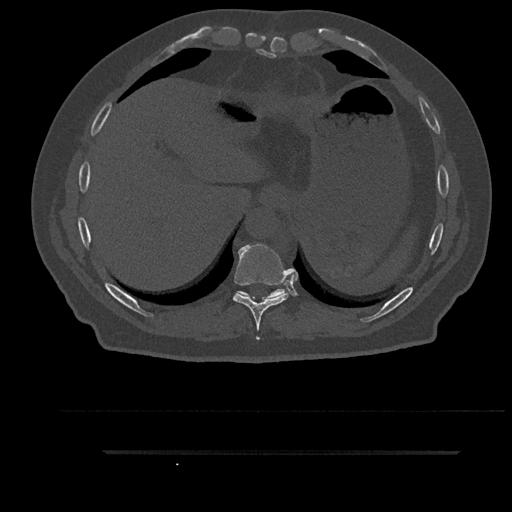
CT including the spine, one axial slice; slice 410 of 797 in the series (ordered by position); bone window (W 1800 / L 400 HU); 0.5 mm slice thickness; 512 × 512 image matrix. Male patient, age 63 years. From the clinical record (not read from this slice): primary cancer: renal; vertebrae with lytic lesions (as recorded): T8.
Annotated regions visible in this slice (semi-automatically segmented with operator editing):
- T10 vertebra: box from (x=237, y=289) to (x=286, y=299) px
- T9 vertebra: (x=233, y=244)–(x=291, y=340)